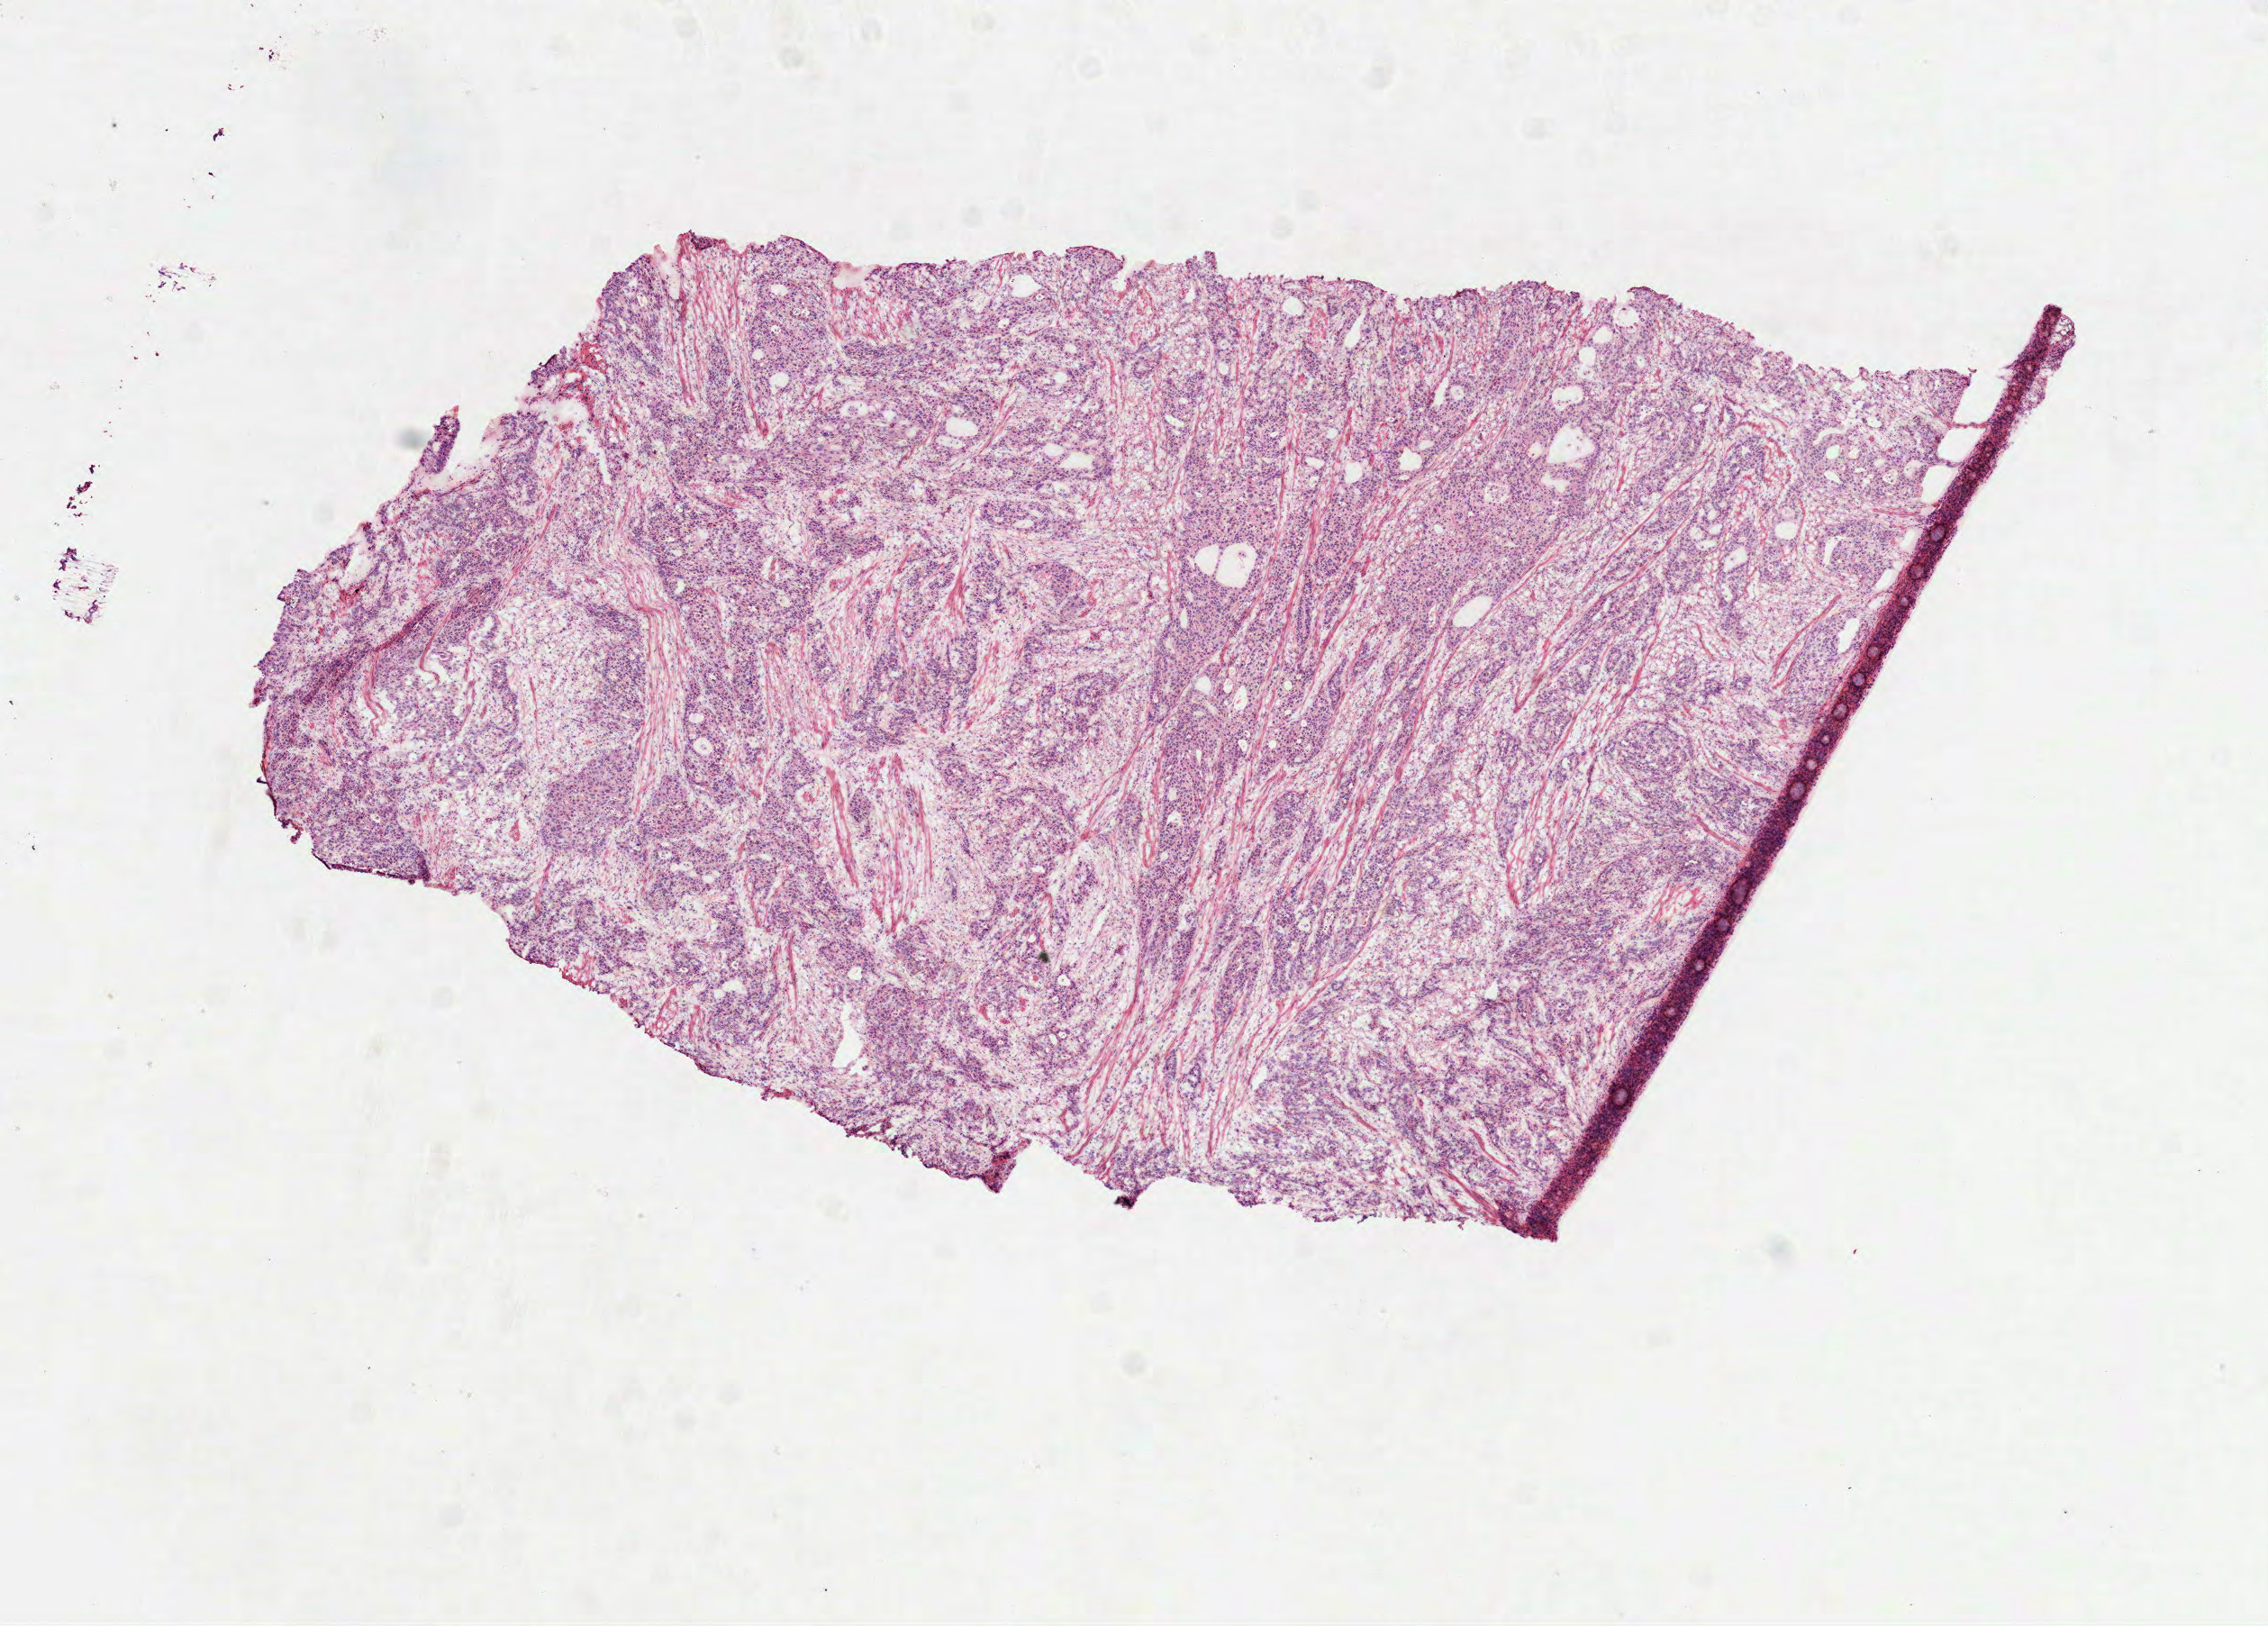
H&E-stained whole-slide image, low-resolution overview of the scanned area, about 10.2 x 7.3 mm; frozen section; sample: primary tumour, stomach. Male patient; age at initial diagnosis 53 years. Histologic grade: G3 (poorly differentiated). Composition of this section per pathologist review: tumour cells 80%, tumour nuclei 80%, normal cells 0%, stromal cells 20%, necrosis 0%.
TNM: T2b N2 M0. Diagnosis: Tubular adenocarcinoma (gastric antrum). Lymph nodes positive (case pathology): 14 of 24 examined. AJCC pathologic stage: IIIA (6th edition).